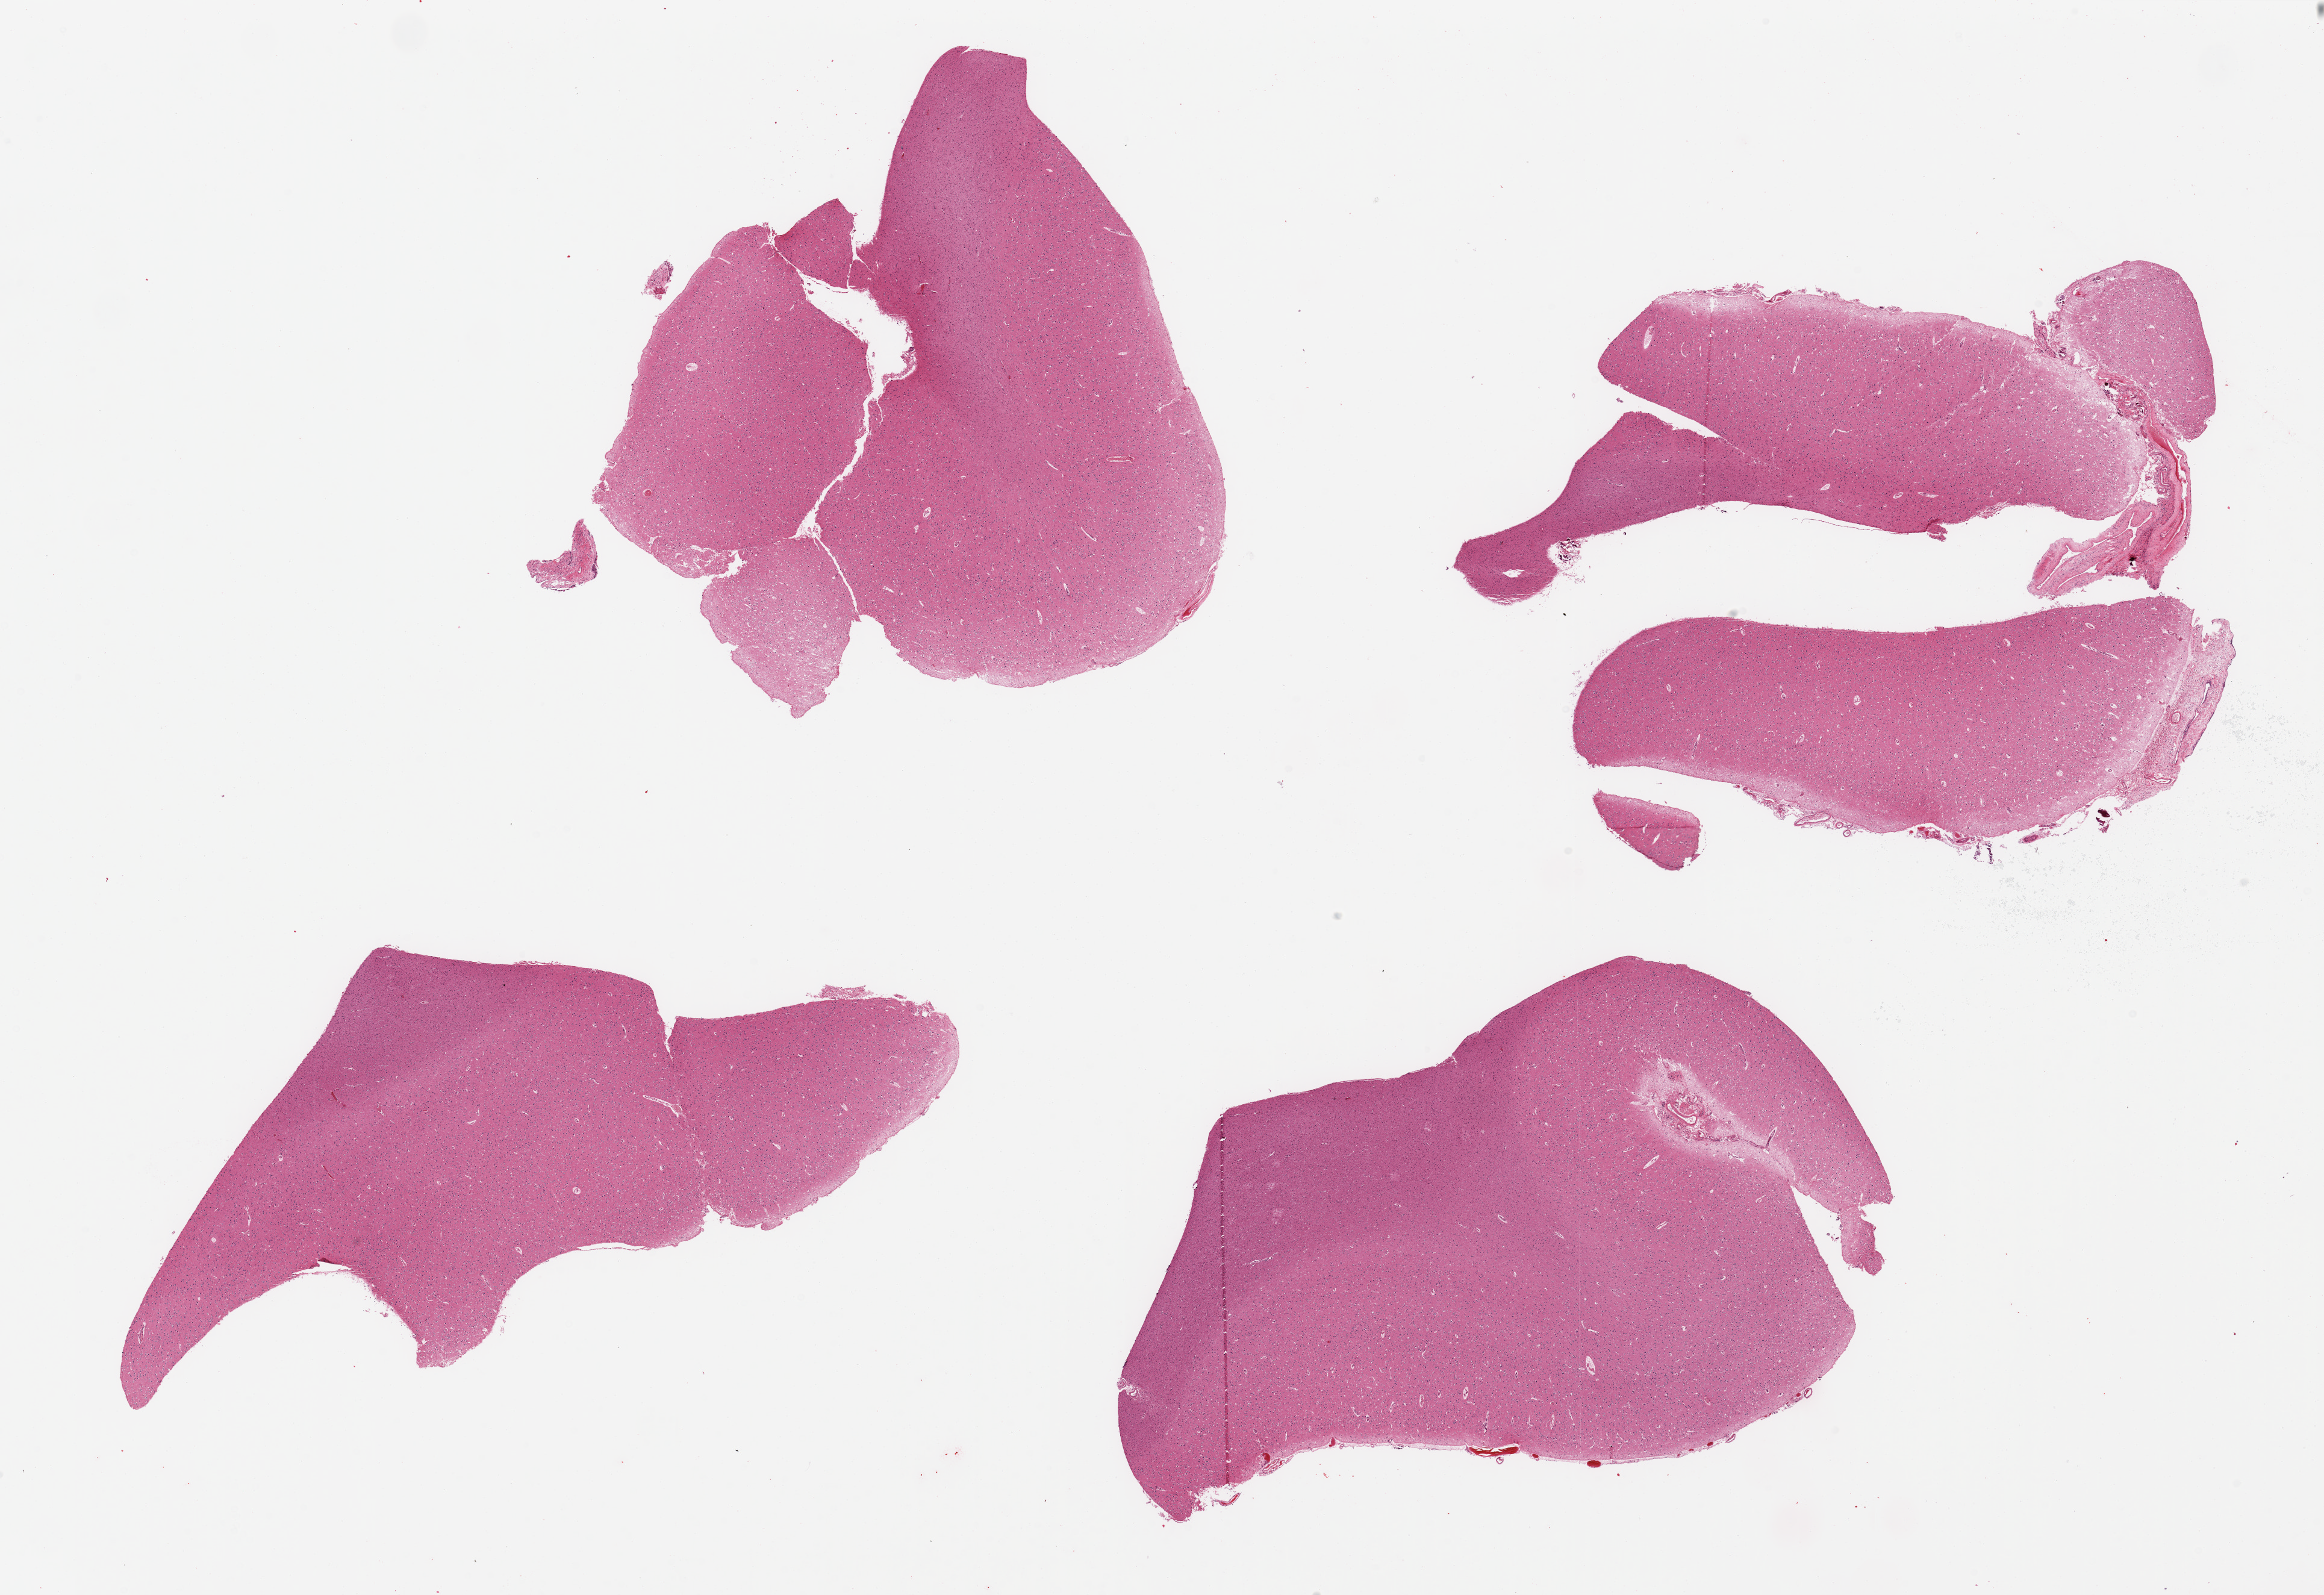
Digitized hematoxylin and eosin (H&E)-stained section — low-resolution overview of the scanned area, about 30.5 x 20.9 mm (acquisition: 20x scan); PAXgene-fixed paraffin-embedded (PFPE) section; sampled site (target tissue): cerebral cortex; donor tissue sample.
- pathologist's review note for this sample: 4 pieces, no abnormalities